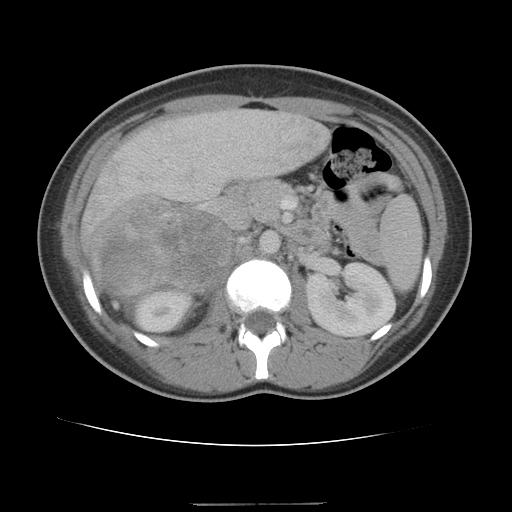
Contrast-enhanced abdominal CT, one axial slice; slice 65 of 100 in the series (ordered by position); 120 kVp; intravenous contrast given; soft-tissue window (W 400 / L 40 HU); 512 × 512 image matrix, field of view 360 × 360 mm. Female patient, age 21 years. Case-level facts recorded for this patient, not image findings: diagnosis: adrenocortical carcinoma; tumour side: right adrenal; tumour size at pathology: 15.5 cm; Ki-67 index: 26 %; stage (as recorded): 3.
Structures marked on this image (semi-automatically segmented with operator editing):
- mass: box from (x=92, y=199) to (x=230, y=295) px